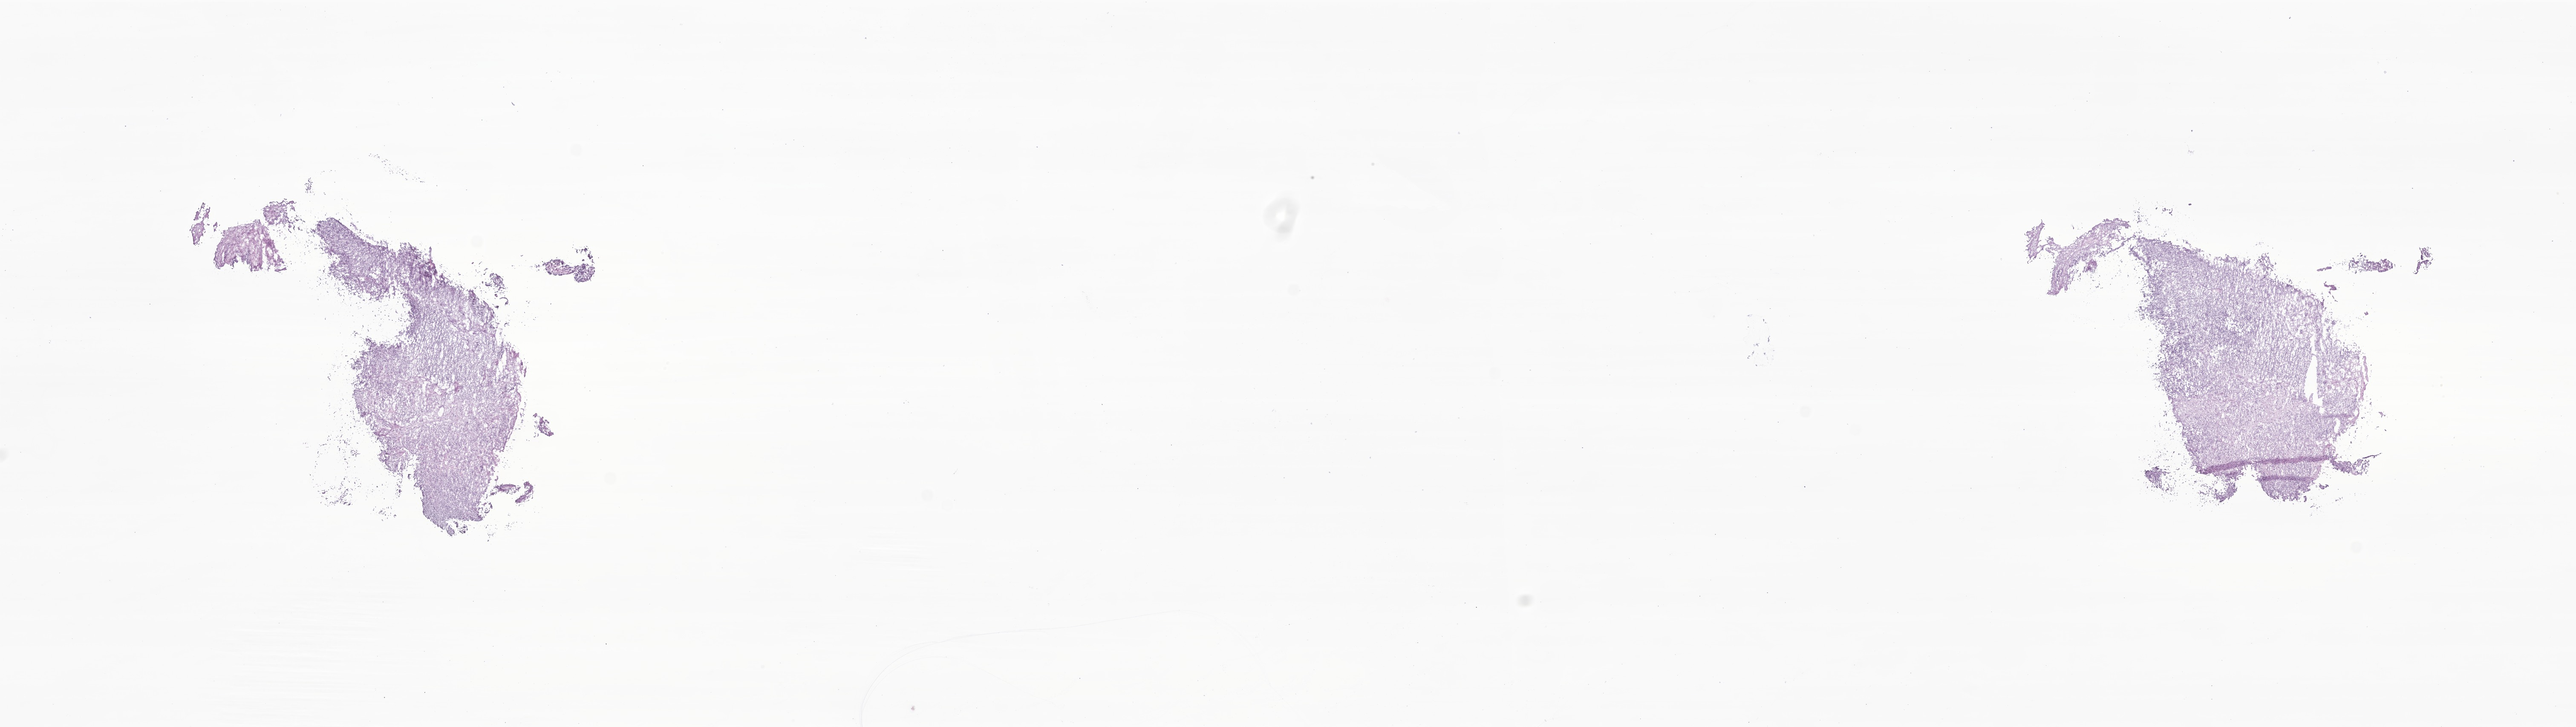
Whole-slide image, H&E stain of tumor tissue from the brain, shown as a low-resolution overview of the whole scanned area (about 25.5 x 7.2 mm); cryosection (OCT / tissue freezing medium). Patient male; age 33 months (2 years 9 months).
Recorded diagnosis: Neoplasm, metastatic.